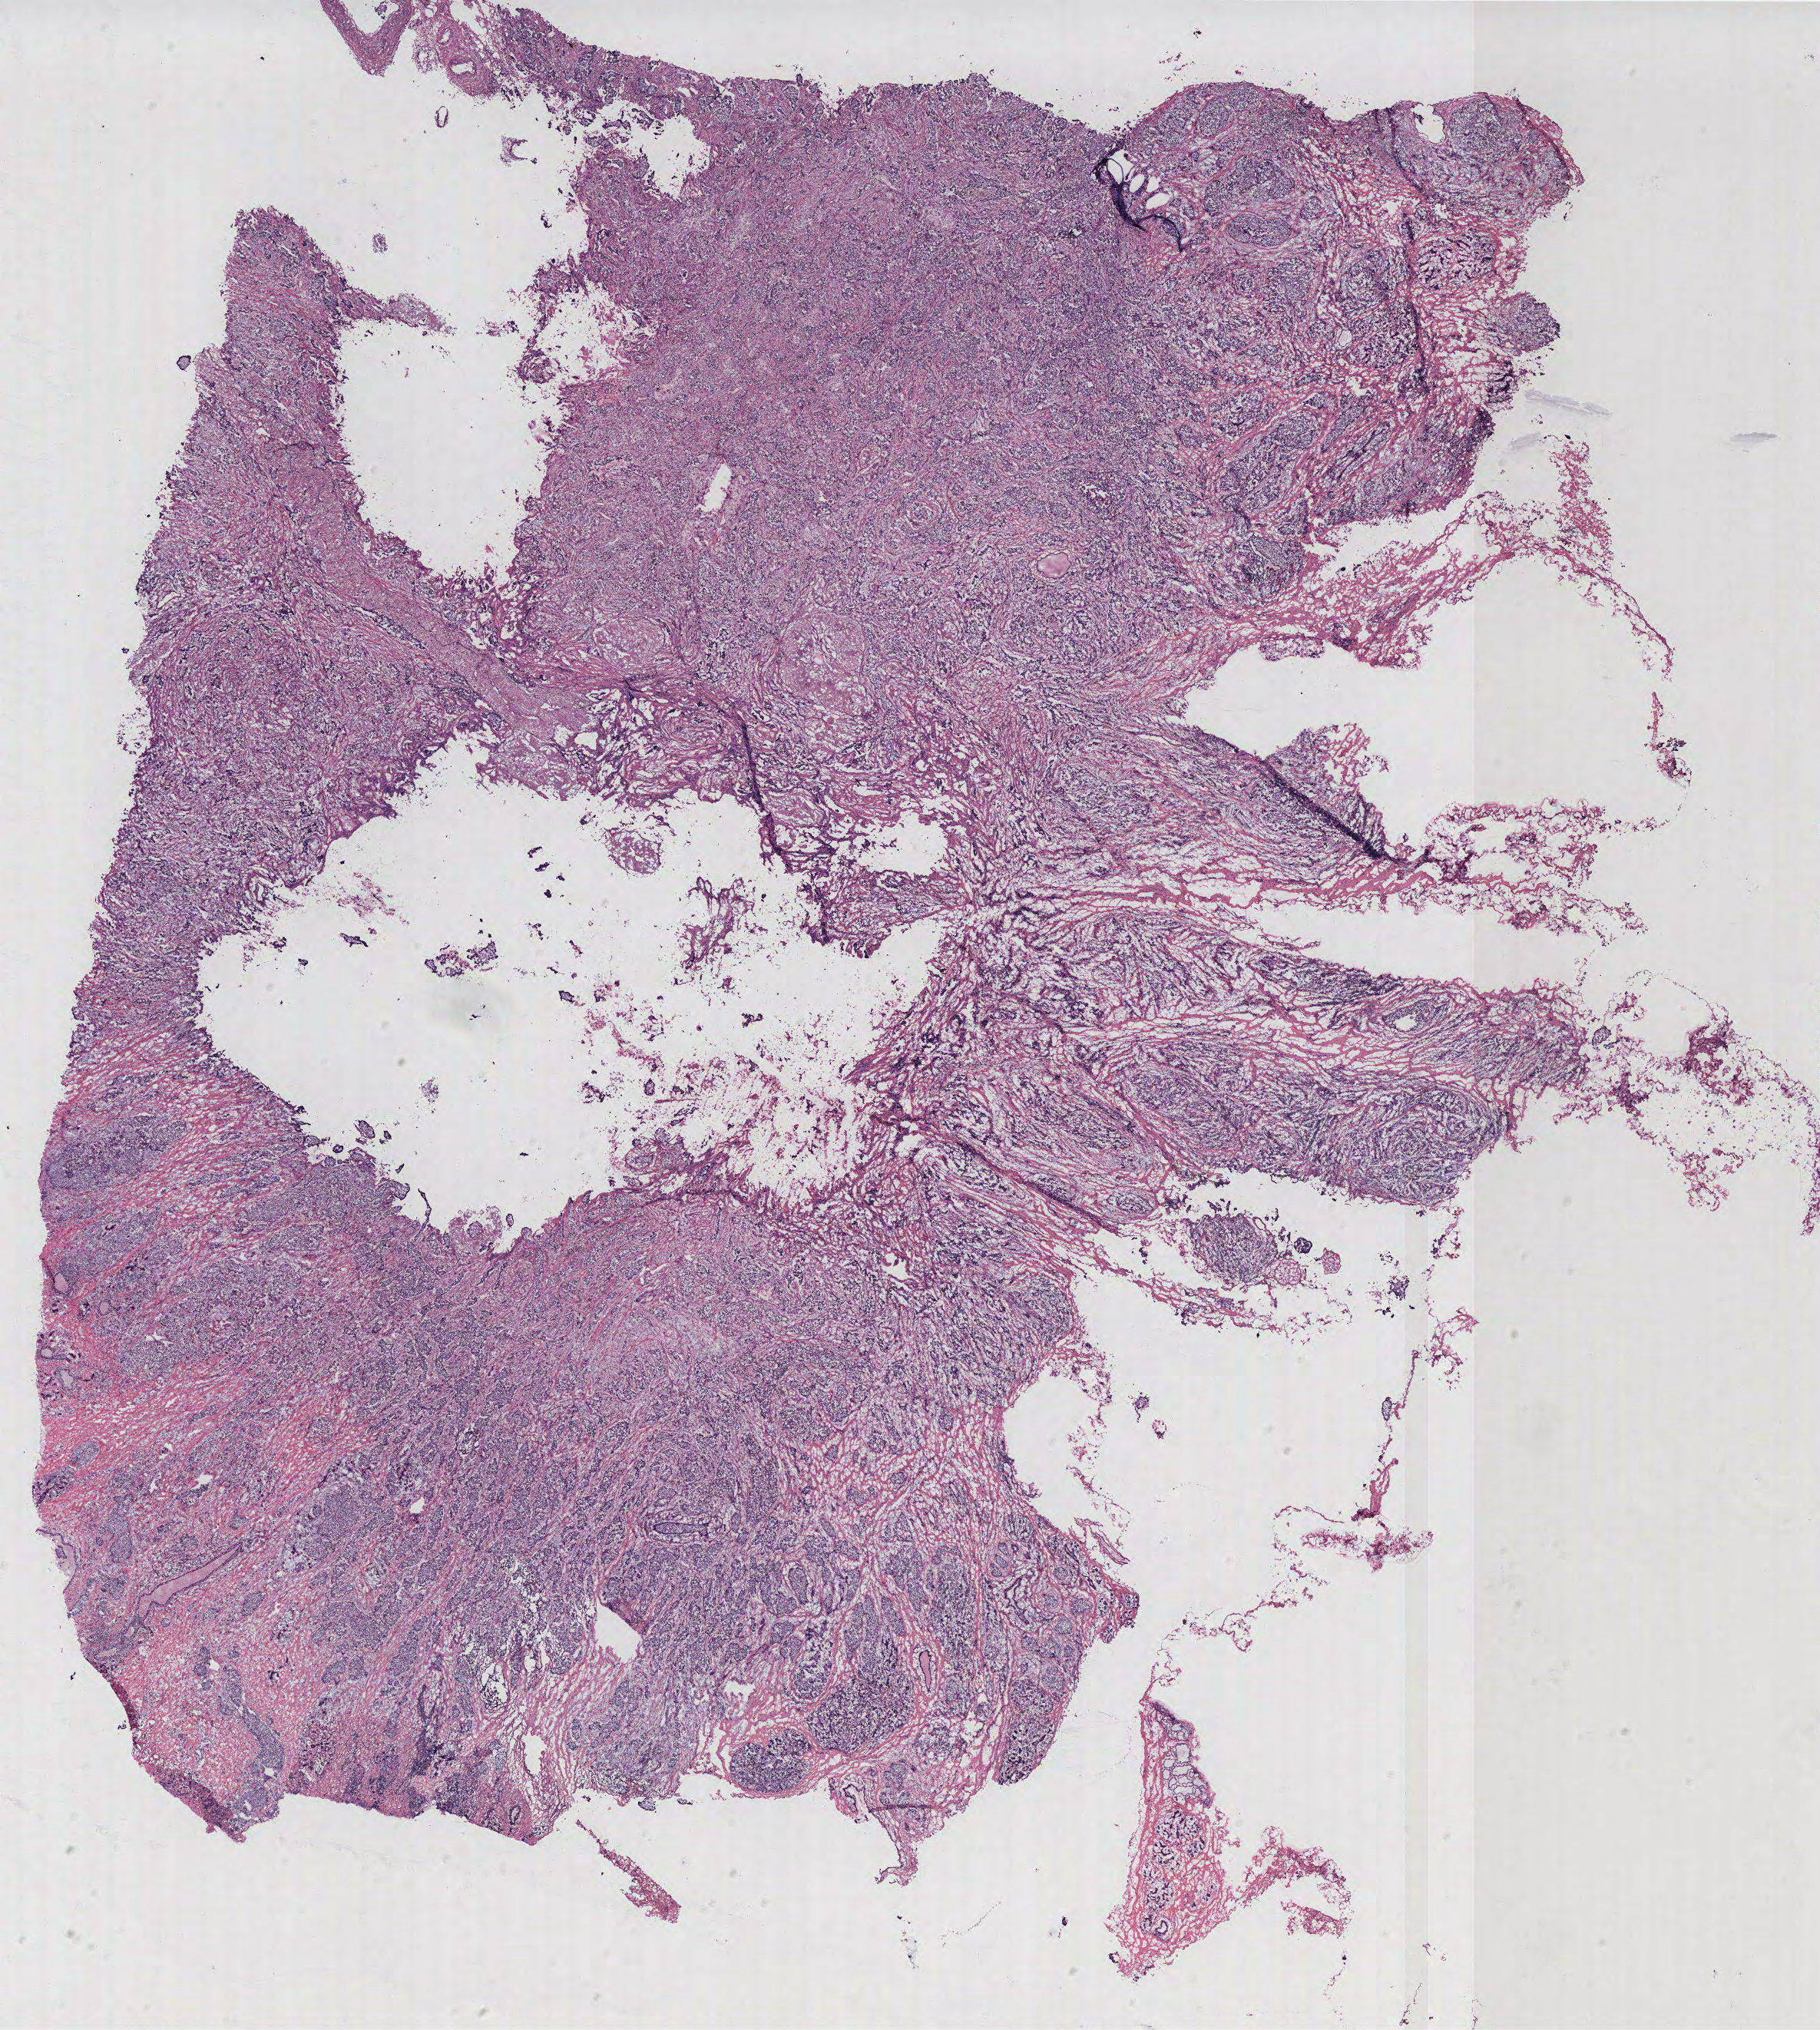
Whole-slide histology image, H&E-stained, low-resolution overview of the scanned area, about 19.0 x 21.2 mm, breast, tissue type not recorded. 52-year-old female patient.
Patient diagnosis: Infiltrating duct carcinoma, NOS.